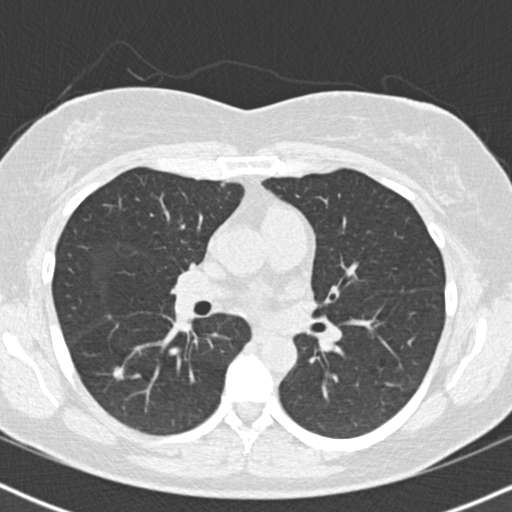
Low-dose screening chest CT, one axial slice. Position 95 of 167 along the scan axis. Reconstruction kernel B30f. Lung window (W 1500 / L -600 HU). 2 mm slice thickness. 512 × 512 image matrix, field of view 320 × 320 mm.
Outlined on this slice (expert manual segmentation):
- lesion 1 (tumor, lower lobe of right lung): bounding box <113,367,124,380> (left, top, right, bottom; pixels)